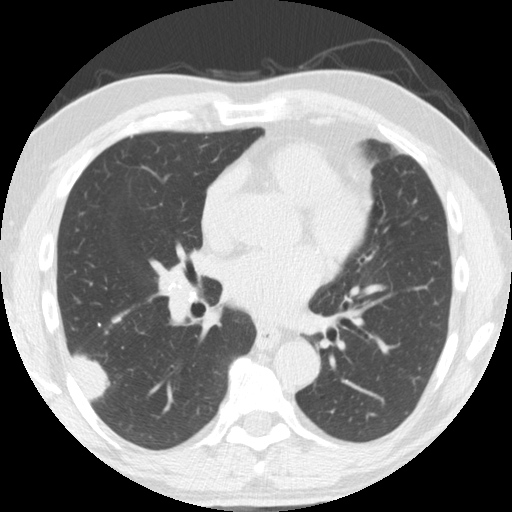
Low-dose screening chest CT, one axial slice. Position 83 of 174 along the scan axis. 120 kVp. Lung window (W 1500 / L -600 HU). 2.5 mm slice thickness. 512 × 512 image matrix, field of view 341 × 341 mm.
Outlined on this slice (expert manual segmentation):
- lesion 1 (tumor, lower lobe of right lung): box from (x=72, y=354) to (x=109, y=401) px